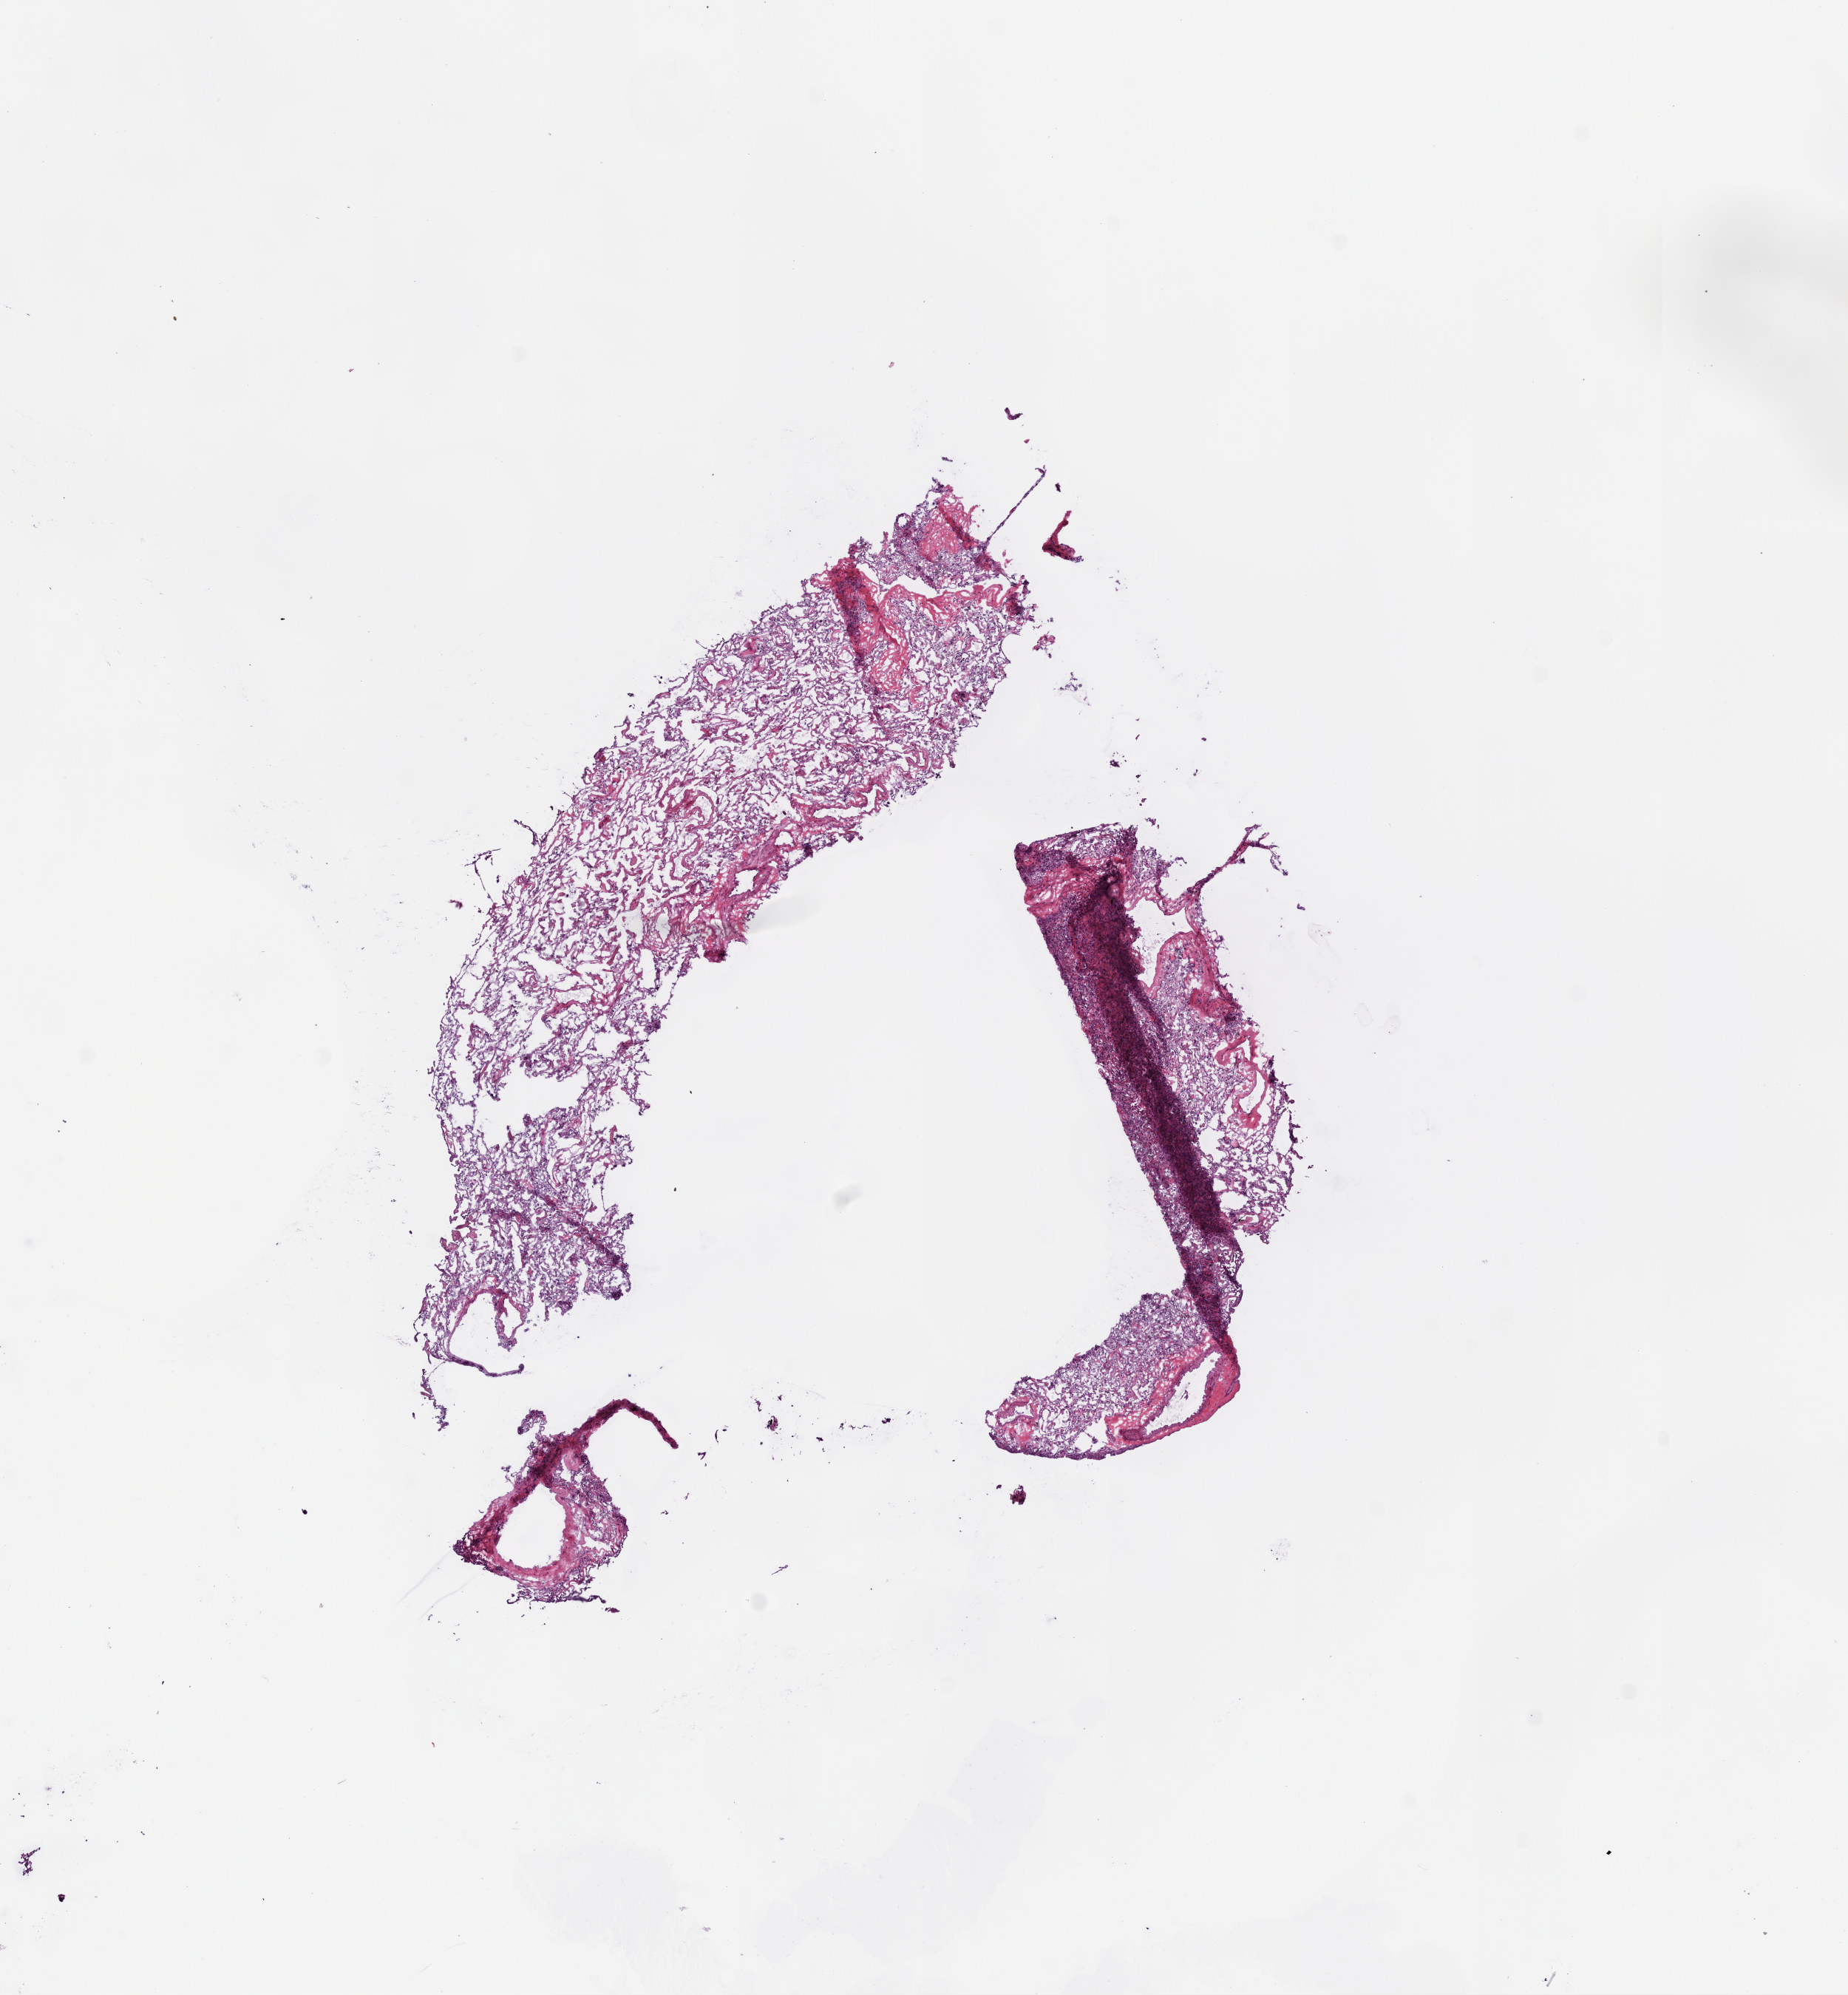
H&E whole-slide image — whole scanned area (about 10.0 x 10.8 mm) shown as a low-resolution overview. Frozen section from the top of the tissue portion. Solid tissue normal (non-tumour tissue) sample from the lung. Female patient; age at initial diagnosis 77 years.
This section: solid tissue normal (non-tumour) sample from the same patient. Patient diagnosis: Squamous cell carcinoma, NOS (lower lobe, lung).